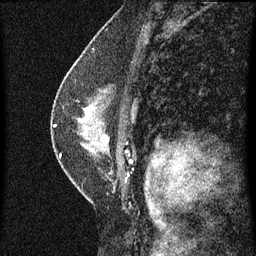
Breast MRI (dynamic contrast-enhanced), one sagittal slice; slice 39 of 60 in the series (ordered by position); dynamic contrast-enhanced series, image 2 of 3 at this slice position (ordered by acquisition); 1.5 T; TE 4.2 ms, TR 8 ms; 2 mm slice thickness; 256 × 256 image matrix, field of view 180 × 180 mm. Female patient, age 47 years.
Annotated regions visible in this slice (semi-automatic segmentation, software-assisted and operator-edited):
- analysis volume of interest (the breast-tissue region the enhancement analysis was run in; not a lesion): bounding box [x1, y1, x2, y2] px = [54, 80, 136, 187]
- tumour enhancement mask (voxels above the 70 % enhancement threshold inside the analysis volume of interest): [55, 126, 132, 161]